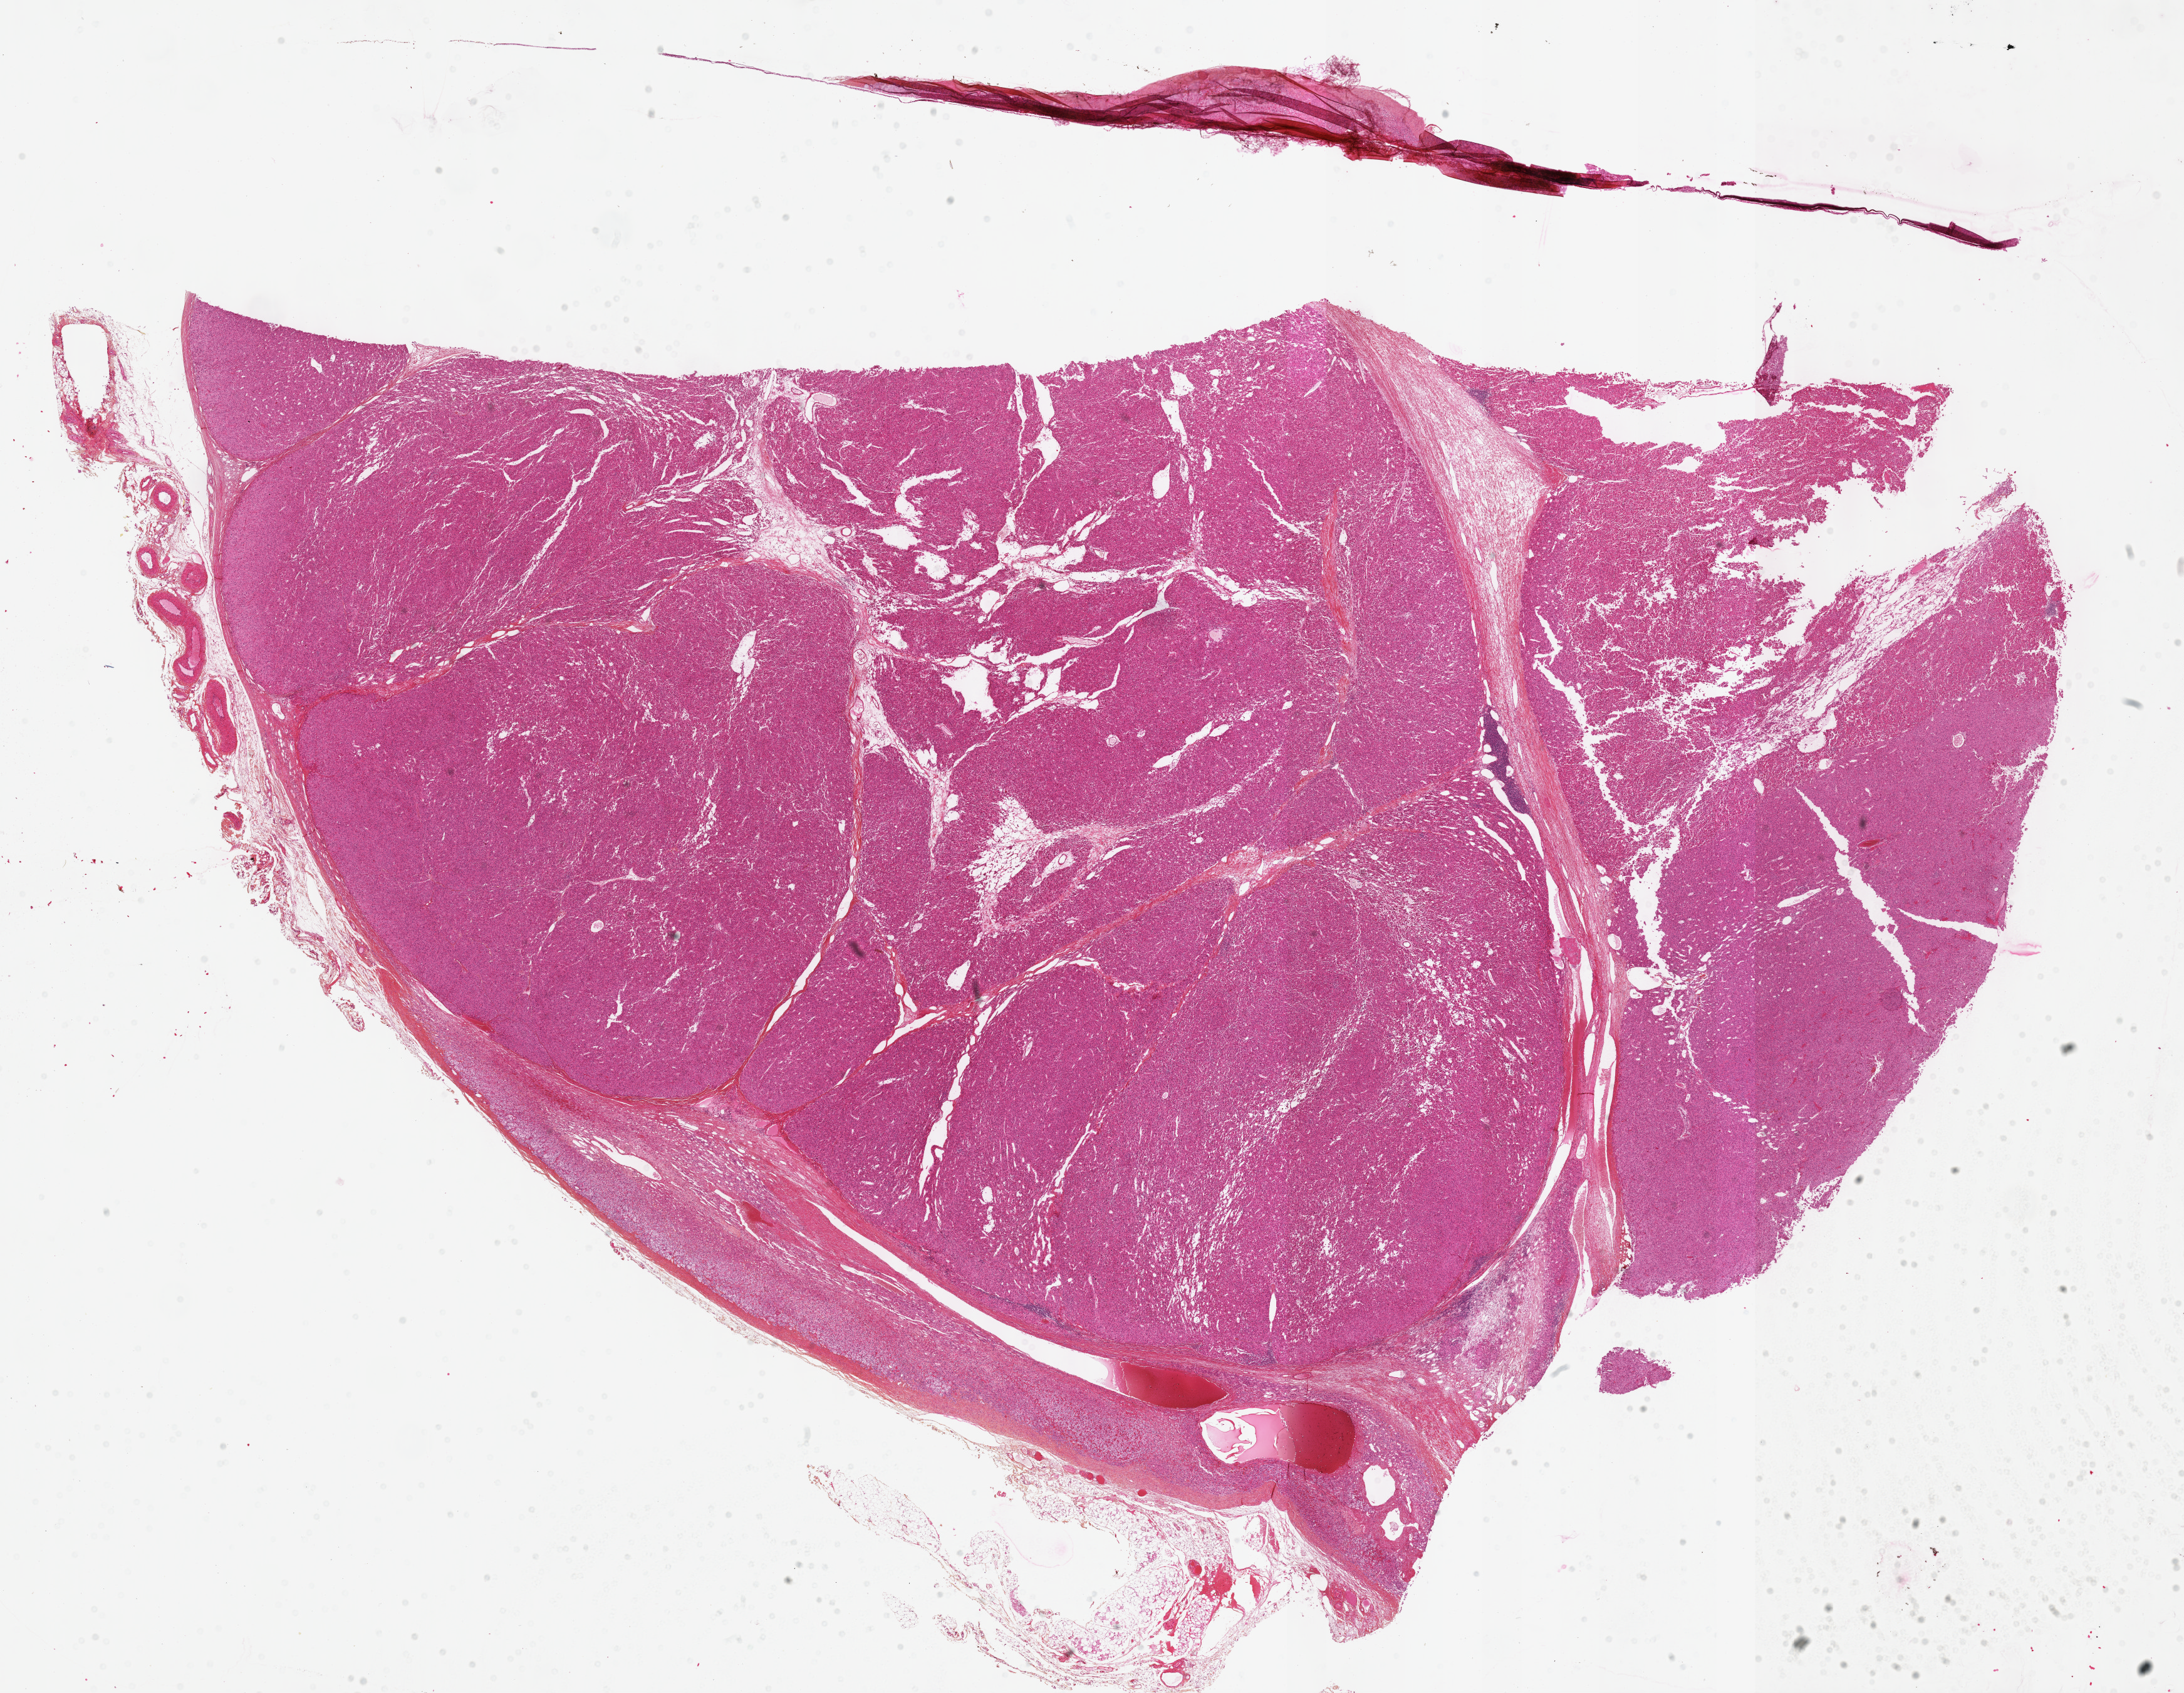
Whole-slide histology image, H&E-stained, shown as a low-resolution overview of the whole scanned area (about 28.2 x 21.8 mm); formalin-fixed paraffin-embedded (FFPE) diagnostic section; adrenal cortex, primary tumour sample. Male, age 62 years at initial diagnosis.
Histologic diagnosis: Adrenal cortical carcinoma (cortex of adrenal gland).